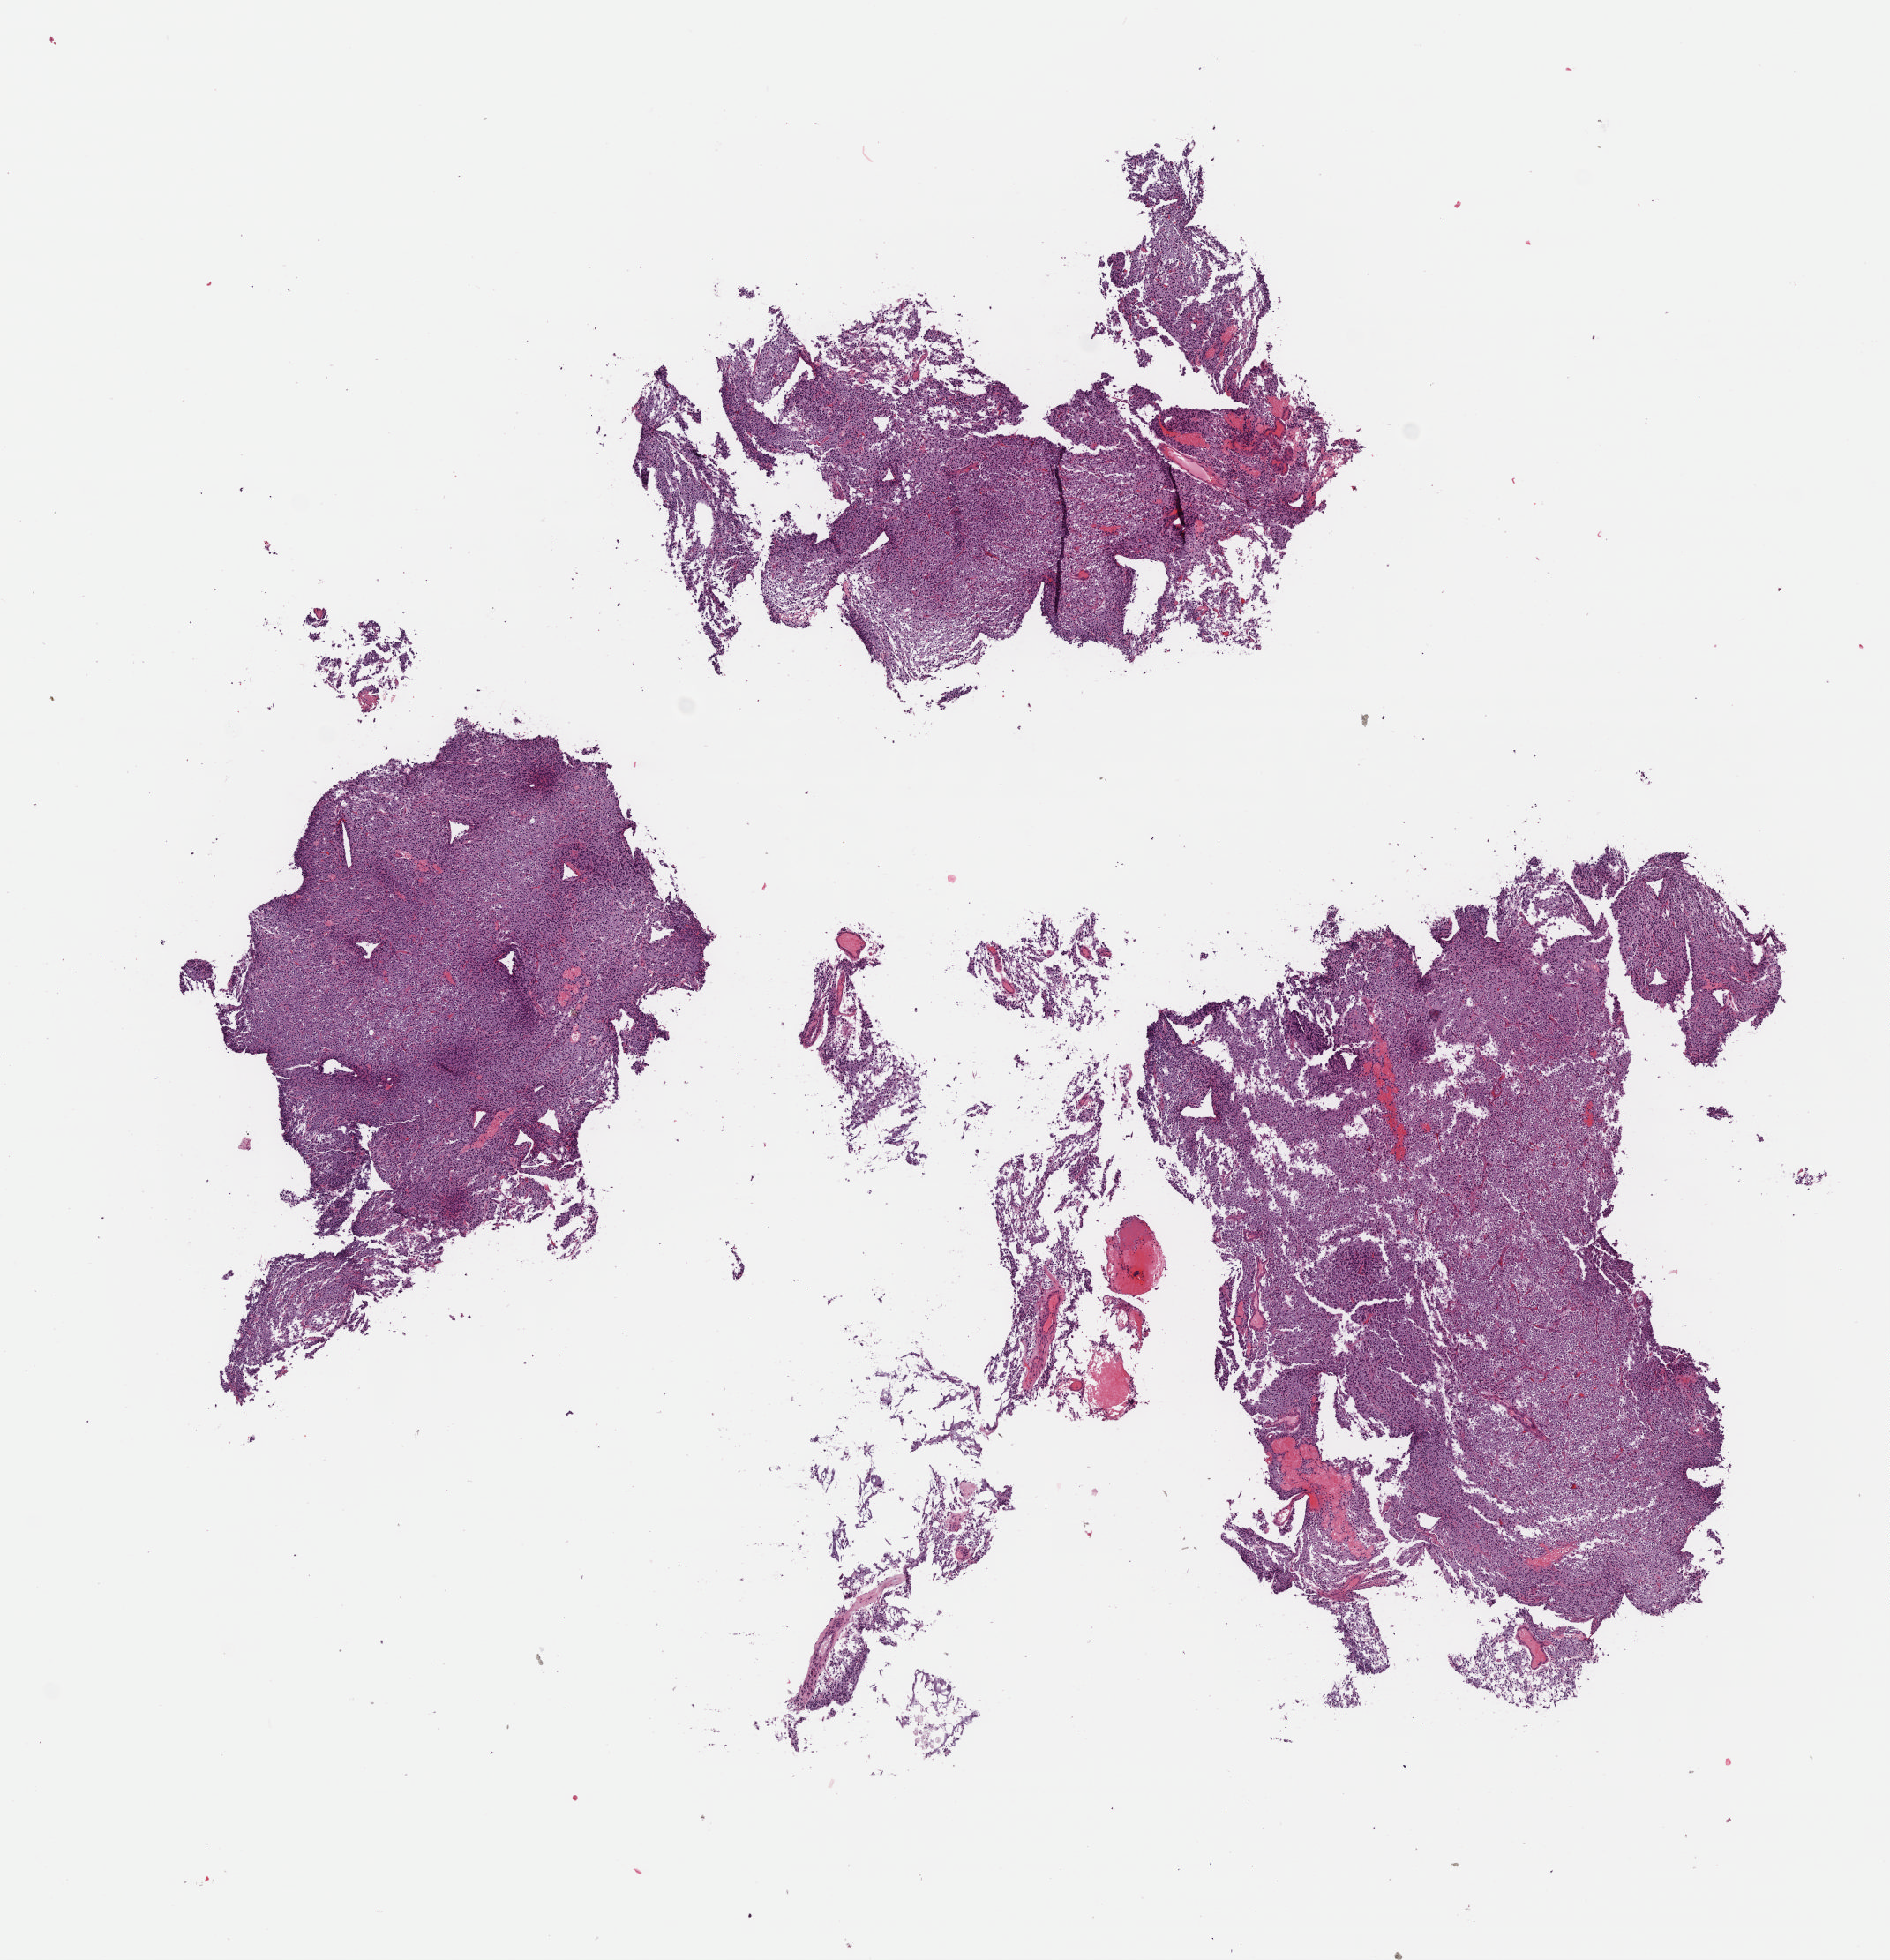
Whole-slide histology image, H&E, whole scanned area (about 8.4 x 8.7 mm, slide scanned at 40x) shown as a low-resolution overview. Formalin-fixed paraffin-embedded (FFPE) diagnostic section. Brain, primary tumour sample. Patient: male, age at initial diagnosis 30 years. Histologic grade: G3 (poorly differentiated).
Laterality: right. Histologic diagnosis: Oligodendroglioma, anaplastic (cerebrum).